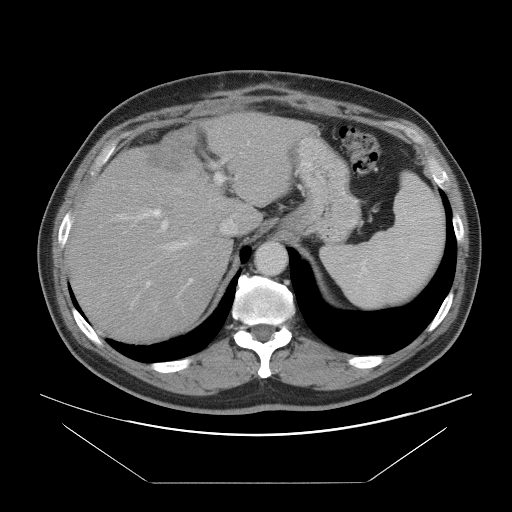
Contrast-enhanced abdominal CT, one axial slice; 120 kVp; intravenous contrast given; soft-tissue window (W 400 / L 40 HU); 5 mm slice thickness; 512 × 512 image matrix. Male patient, age 62 years. Case-level facts recorded for this patient, not image findings: diagnosis: colorectal cancer liver metastases, imaged before liver resection; multiple liver metastases: no.
Outlined on this slice (manually delineated by an expert):
- hepatic veins: bounding box <157,139,285,256> (left, top, right, bottom; pixels)
- liver: <71,113,305,339>
- planned liver remnant (the part of the liver to remain after resection): <71,169,232,338>
- portal vein (with intrahepatic branches): <117,142,249,305>
- liver metastasis: <146,131,193,171>